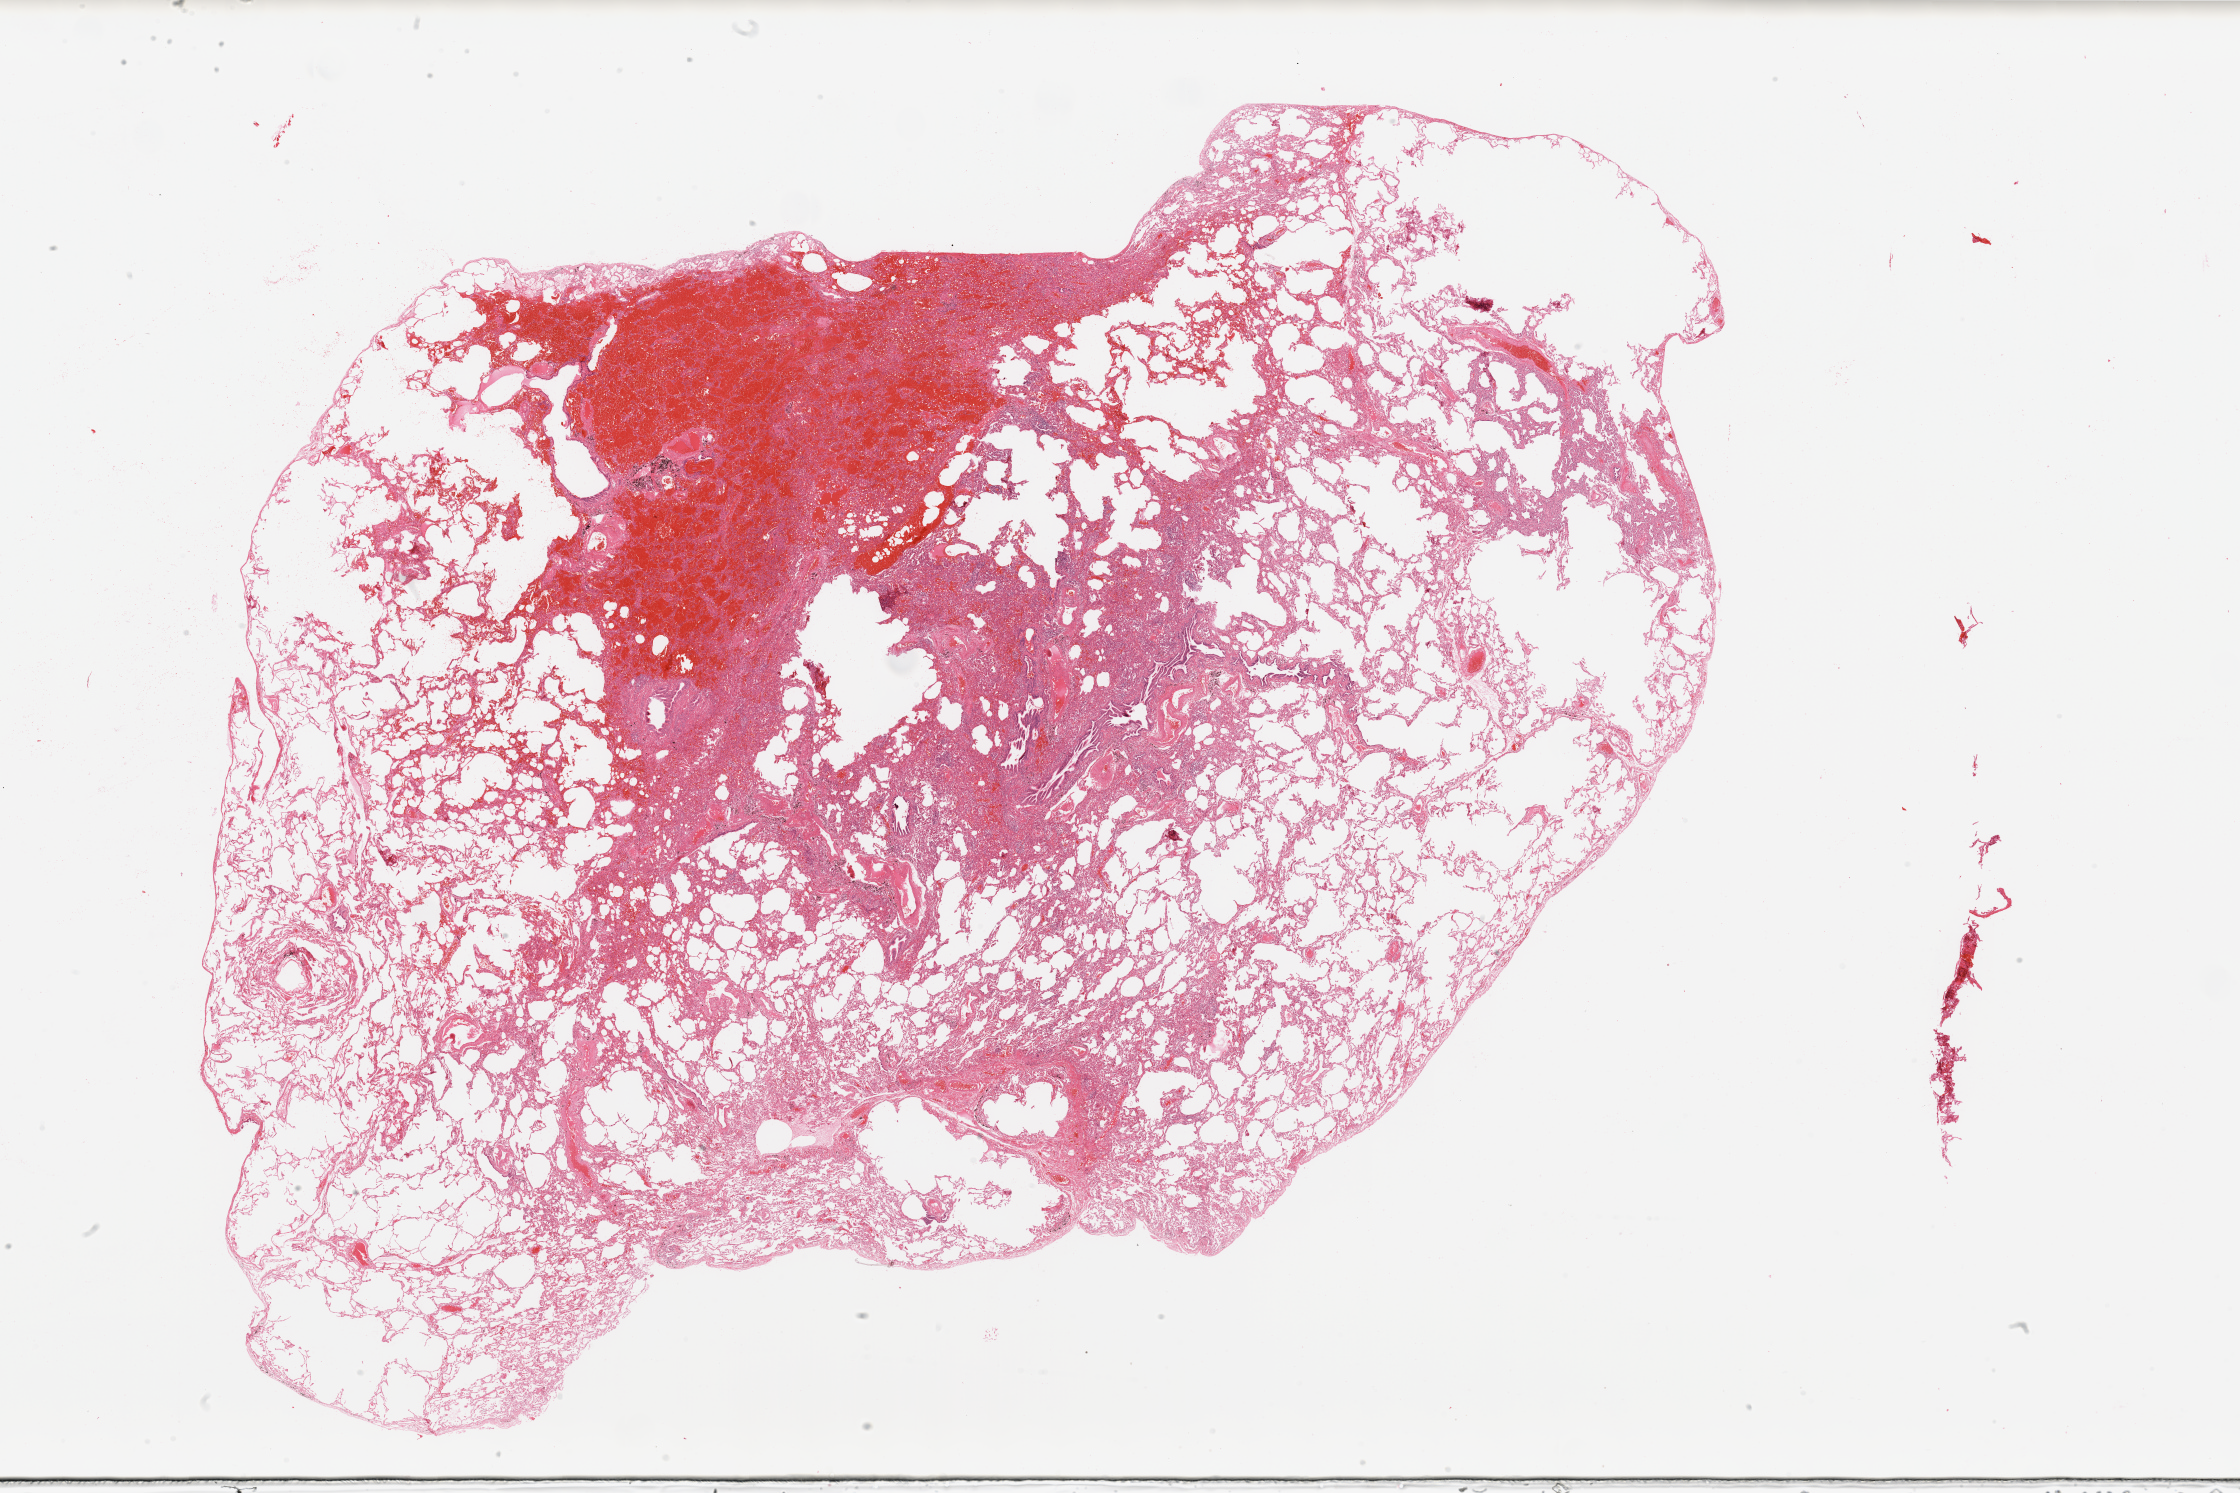
Whole-slide histology image, H&E-stained — low-resolution overview of the scanned area, about 35.4 x 23.6 mm; normal (non-tumour) tissue sample, sampled site: lung. 67-year-old male patient.
This section: normal (non-tumour) tissue from the same patient. Patient diagnosis: Adenocarcinoma, NOS.